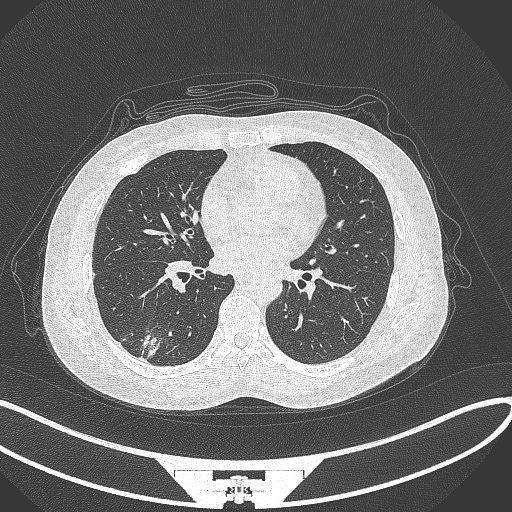
Chest CT, one axial slice; position 133 of 352 along the scan axis; reconstruction kernel B70f; lung window (W 1500 / L -600 HU); 1 mm slice thickness; 512 × 512 image matrix, field of view 400 × 400 mm. Patient: female, 55 years. From the clinical record (not read from this slice): clinical TNM (as recorded): T1c N1 M0.
Annotated regions visible in this slice (rectangle marked by the reading radiologist):
- lung tumour (recorded histology: adenocarcinoma): bounding box <138,328,162,363> (left, top, right, bottom; pixels)